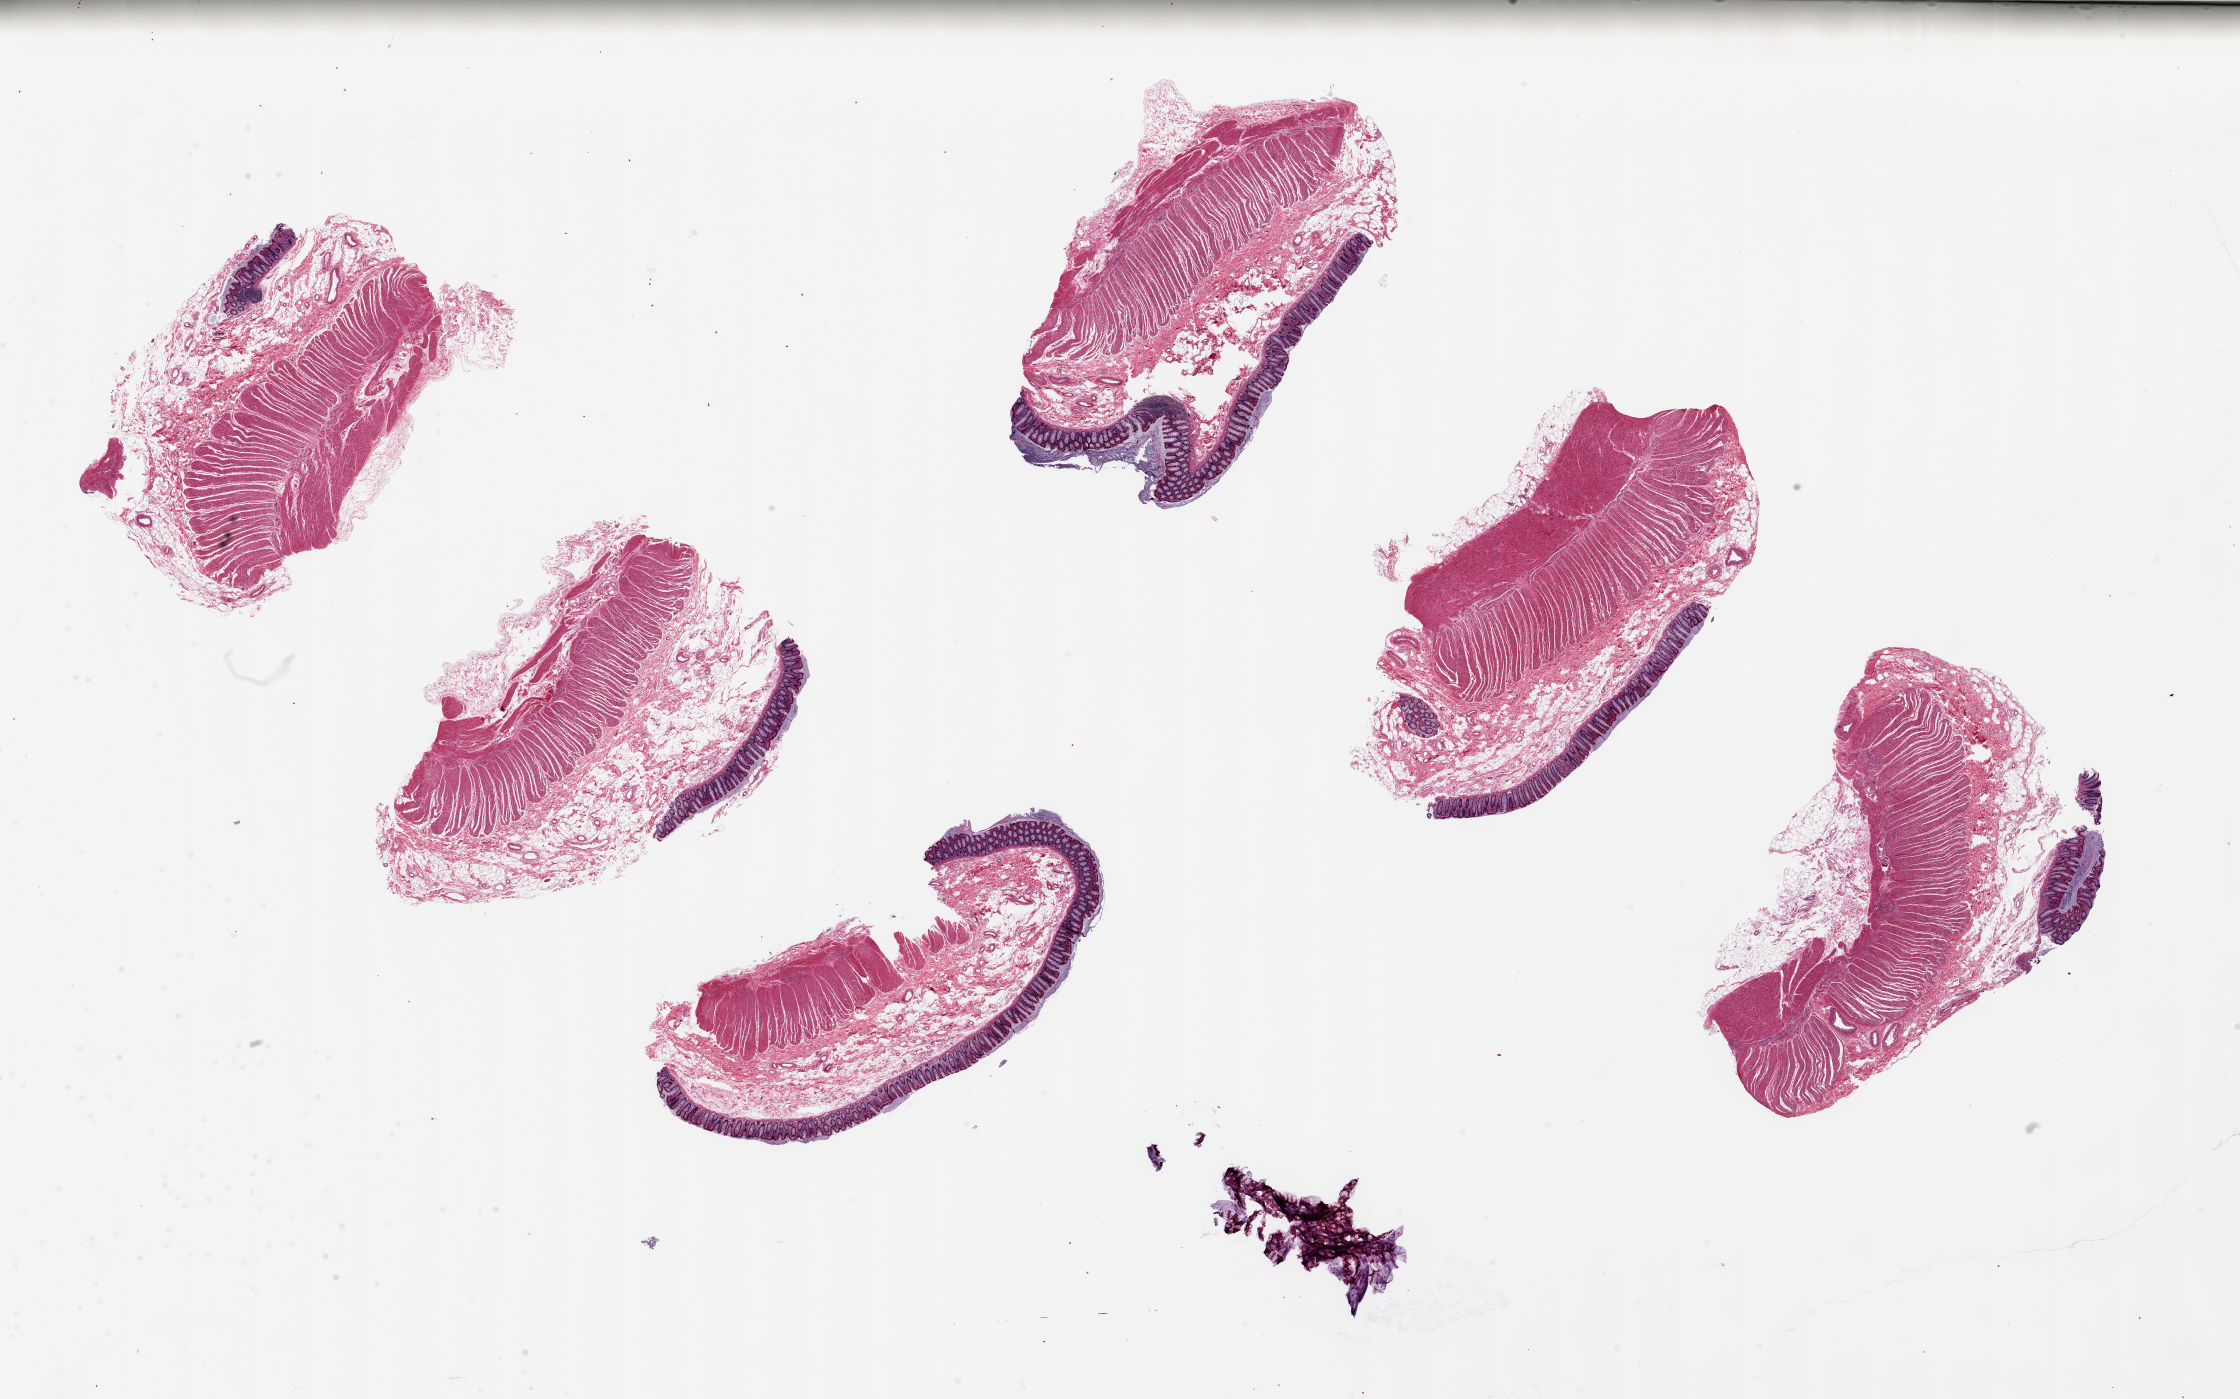
Whole-slide image, hematoxylin and eosin (H&E) stain, whole scanned area (about 35.4 x 22.1 mm) shown as a low-resolution overview. PAXgene-fixed, paraffin-embedded tissue. Sampled site (target tissue): transverse colon. Donor tissue sample. Donor sex: male.
Pathologist's review note for this sample: 6 pieces ~7x3mm. Mucosa/epithelium well-preserved, ~10% of thickness.